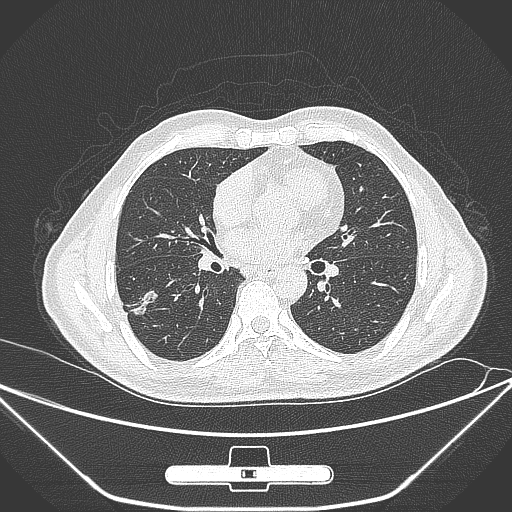
Chest CT, one axial slice. Lung window (W 1500 / L -600 HU). 512 × 512 image matrix, field of view 398 × 398 mm. Male patient, age 71 years. From the clinical record (not read from this slice): clinical TNM (as recorded): T1c N0 M0; histopathological grade: G2.
Annotated regions visible in this slice (bounding box drawn by a radiologist):
- lung tumour (recorded histology: adenocarcinoma): bounding box (x1, y1, x2, y2) in pixels: (122, 281, 159, 321)